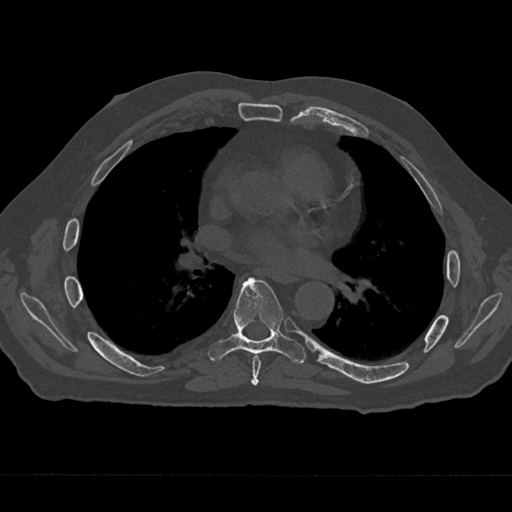
CT including the spine, one axial slice; position 378 of 797 along the scan axis; bone window (W 1800 / L 400 HU); 0.5 mm slice thickness; 512 × 512 image matrix, field of view 377 × 377 mm. Male patient, age 75 years. Case-level facts recorded for this patient, not image findings: primary cancer: renal; vertebrae with lytic lesions (as recorded): T4.
Structures marked on this image (semi-automatically segmented with operator editing):
- T6 vertebra: bounding box [x1, y1, x2, y2] px = [251, 354, 261, 386]
- T7 vertebra: [208, 277, 306, 364]